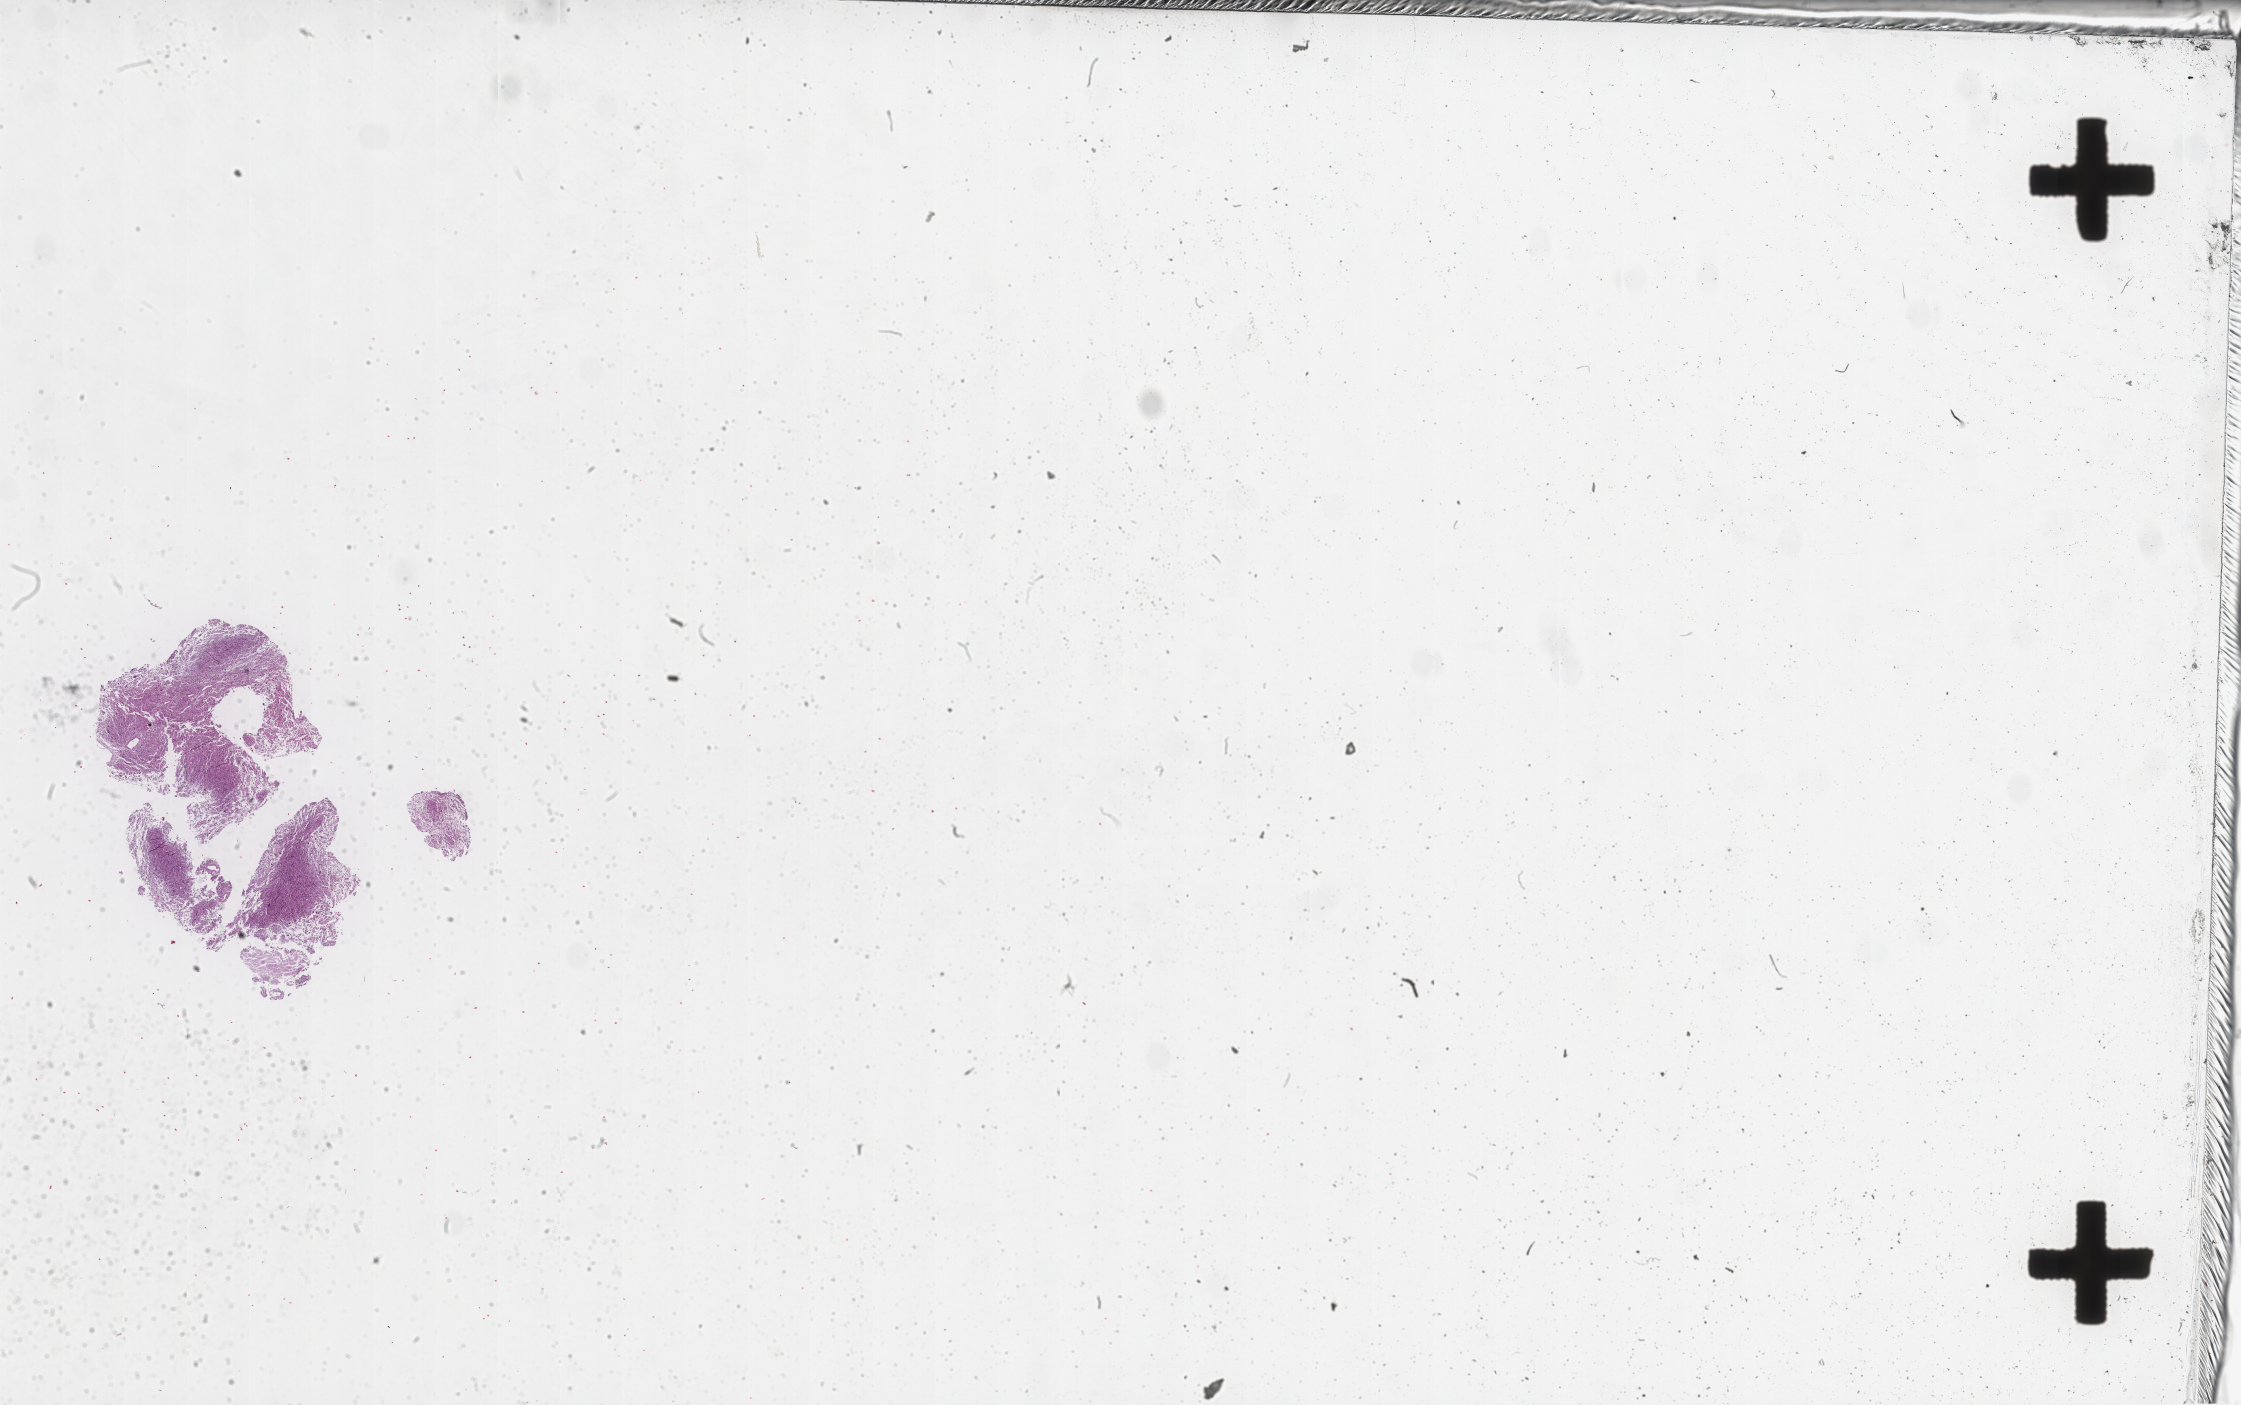
Hematoxylin and eosin (H&E) stained whole-slide image, whole scanned area (about 36.1 x 22.6 mm, from a 20x scan) shown as a low-resolution overview. Tumour tissue sample, sampled site: frontal lobe. Male, 31 y/o. Pathologist review of this section (percent, as recorded): tumour nuclei 65%, necrosis 10%.
Histologic diagnosis: Glioblastoma.